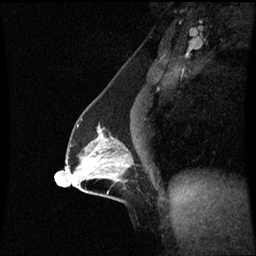
Breast MRI (dynamic contrast-enhanced), one sagittal slice. Slice 37 of 60 in the series (ordered by position). Dynamic contrast-enhanced series, image 2 of 3 at this slice position (ordered by acquisition). 1.5 T. TE 4.2 ms, TR 8.9 ms. 256 × 256 image matrix. Female patient, age 47 years. Case-level facts recorded for this patient, not image findings: setting: breast cancer imaged before/during neoadjuvant chemotherapy; receptor status: HR-positive, HER2-negative.
Structures marked on this image (semi-automatically segmented with operator editing):
- analysis volume of interest (the breast-tissue region the enhancement analysis was run in; not a lesion): box from (x=64, y=124) to (x=135, y=196) px
- tumour enhancement mask (voxels above the 70 % enhancement threshold inside the analysis volume of interest): (x=101, y=135)–(x=104, y=137)